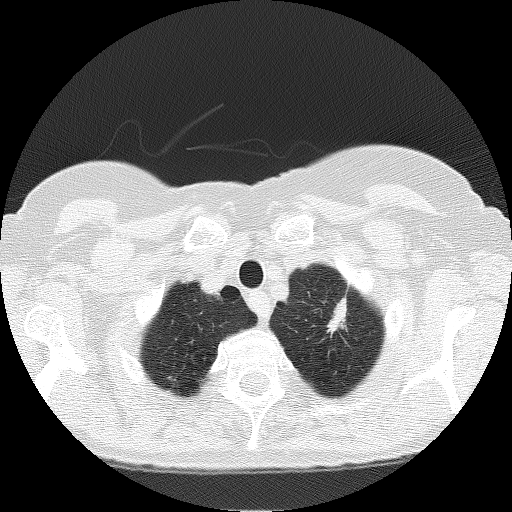
Axial slice from a low-dose chest CT screening exam; first (baseline) screen; lung window (W 1500 / L -600 HU); 2 mm slice thickness; lung (sharp) reconstruction kernel (FC51); 120 kVp; slice 14 of 166 in the series. Female participant, aged 66 years at enrolment. Current smoker at enrolment.
Expert-annotated lung lesion, bounding box [x1, y1, x2, y2] px = [313, 288, 367, 344]. The screening reader recorded 3 non-calcified nodules or masses ≥4 mm on this exam; which of them this box marks is not recorded. Official screen result: positive, change unspecified: nodule(s) >= 4 mm or enlarging nodule(s), mass(es), or other non-specific abnormalities suspicious for lung cancer. Participant outcome: lung cancer diagnosed 156 days after this screen — adenocarcinoma, NOS, left upper lobe, moderately differentiated (G2), stage IB (AJCC 6th edition), 17 mm at pathology.